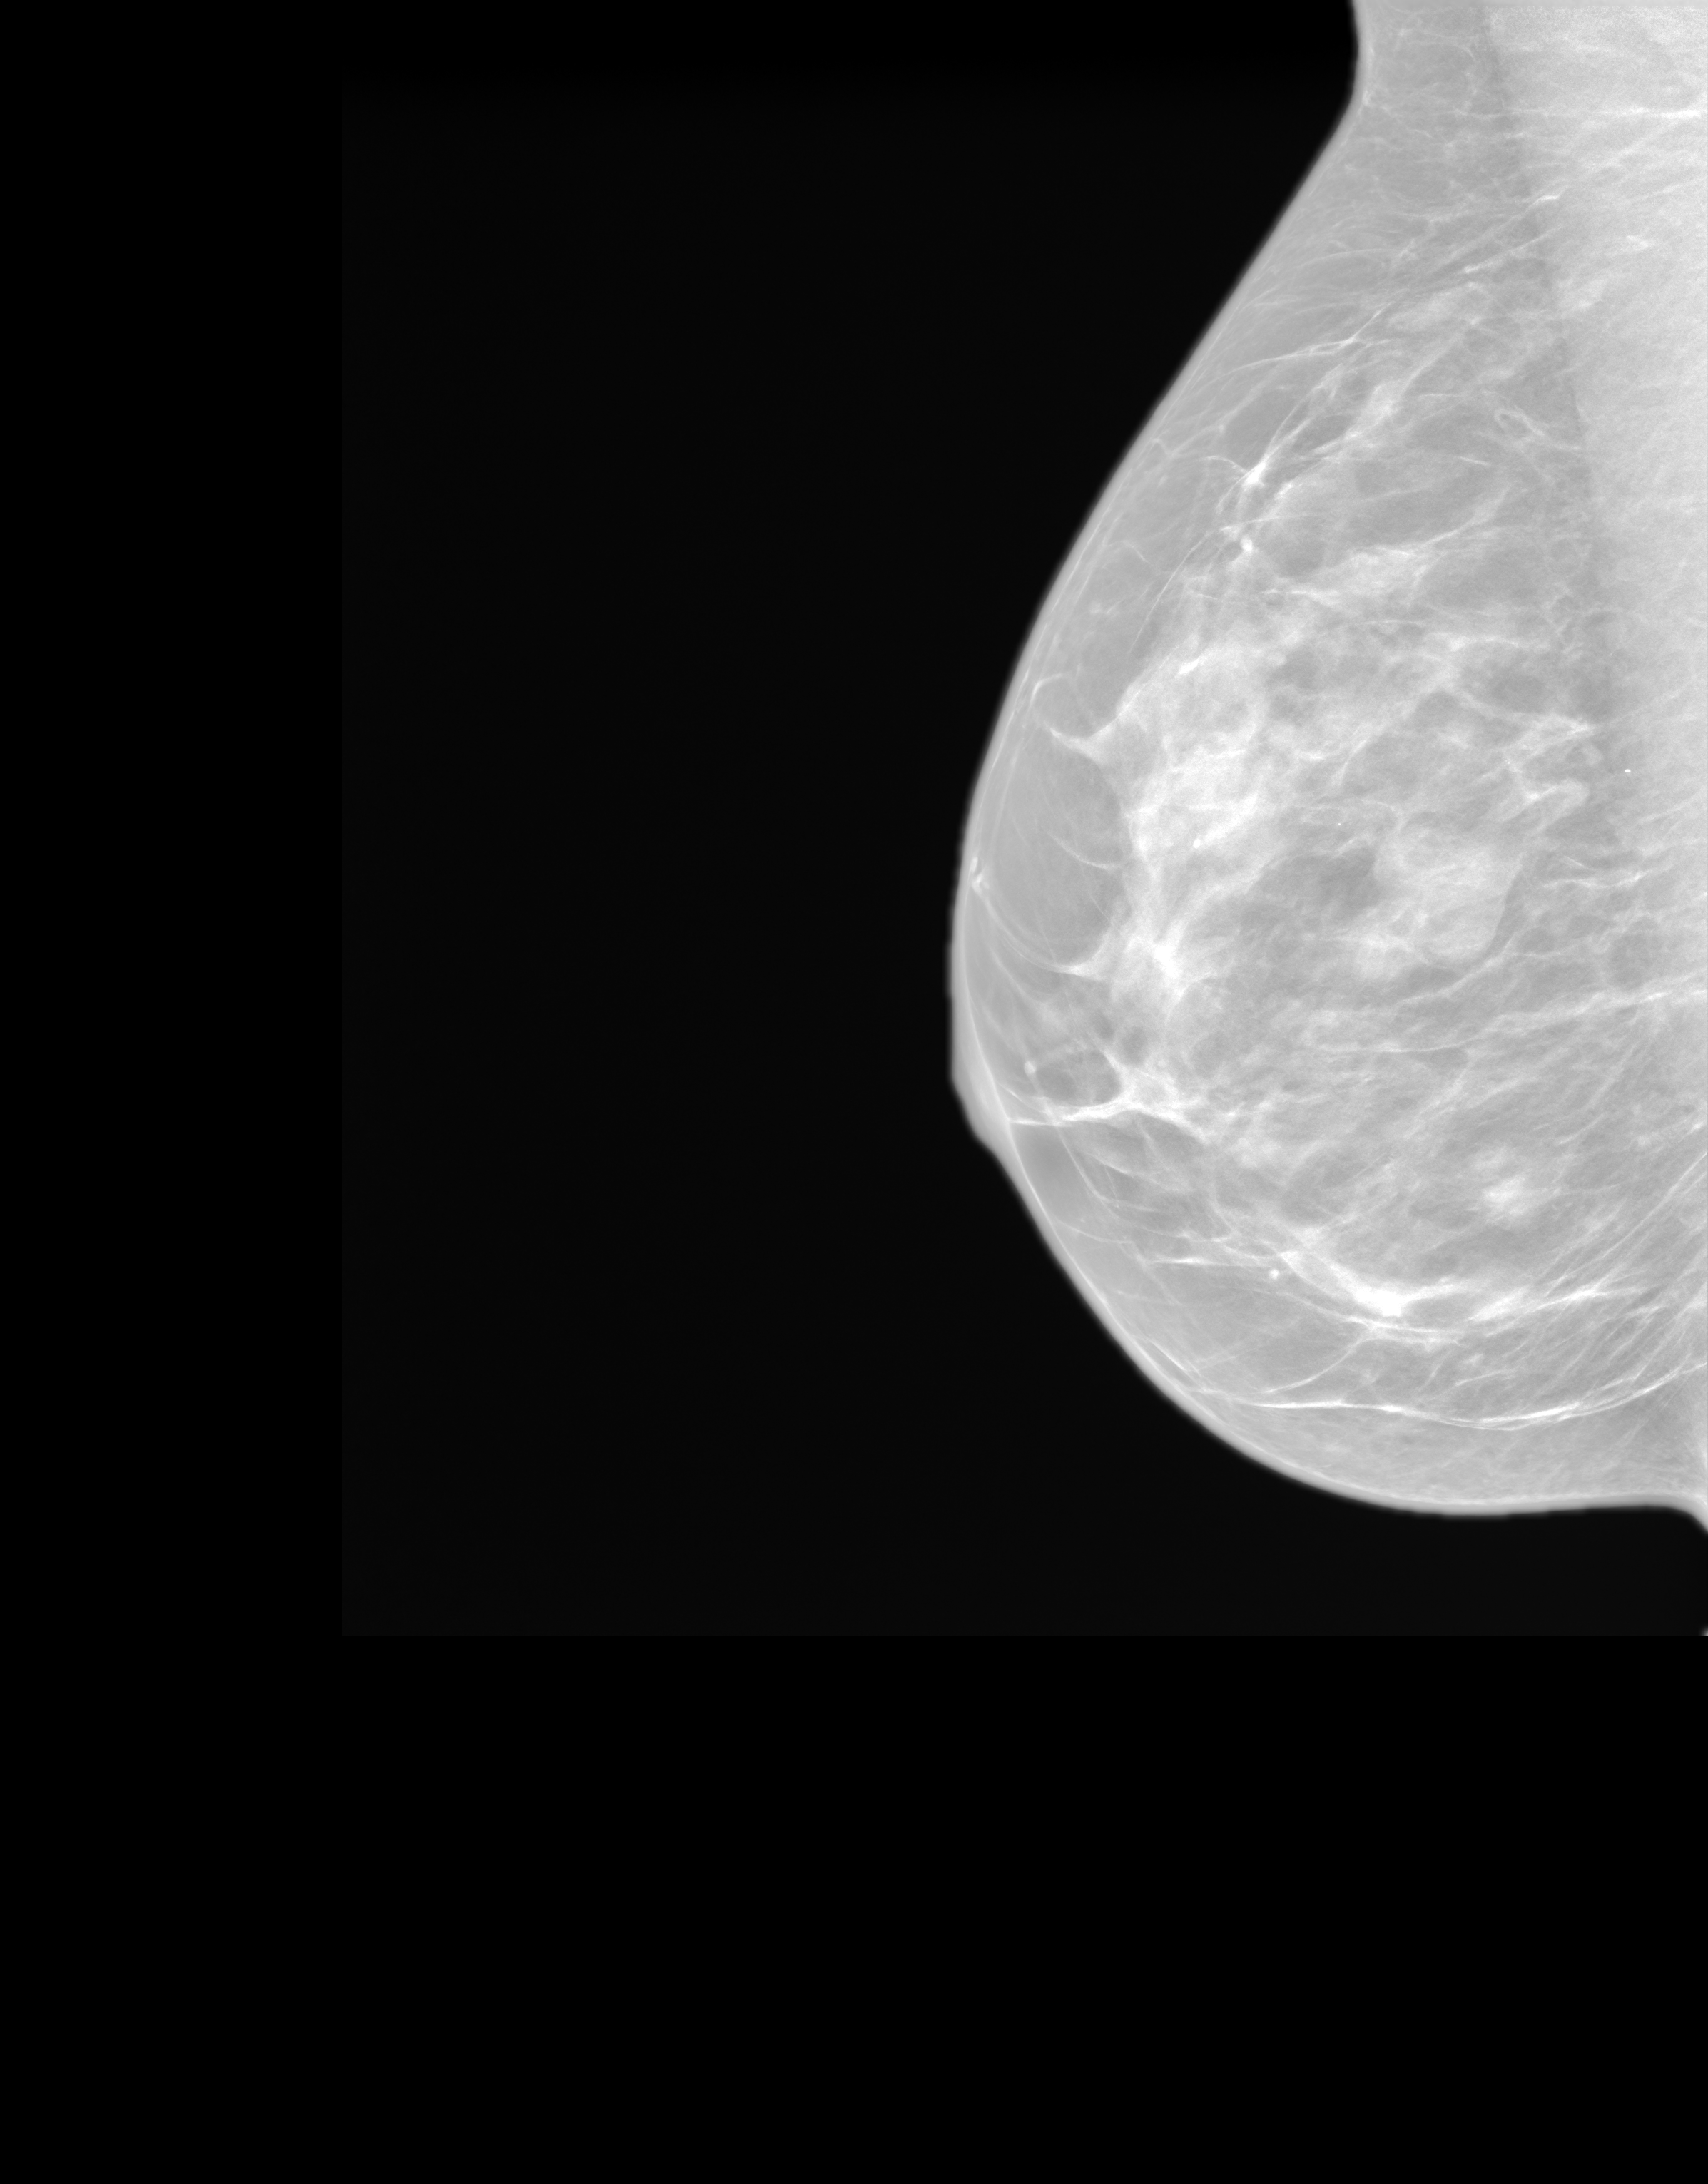
Synthetic 2-D view generated from a tomosynthesis acquisition (not an FFDM exposure); right breast; mediolateral oblique (MLO) view; screening examination. Patient: female, 51 years.
BI-RADS breast density category at the screening exam (both breasts, scale 1–4): 3. Final BI-RADS category for the screening round (tomosynthesis exam, both breasts): category 2. Recall: no recall after this screen.